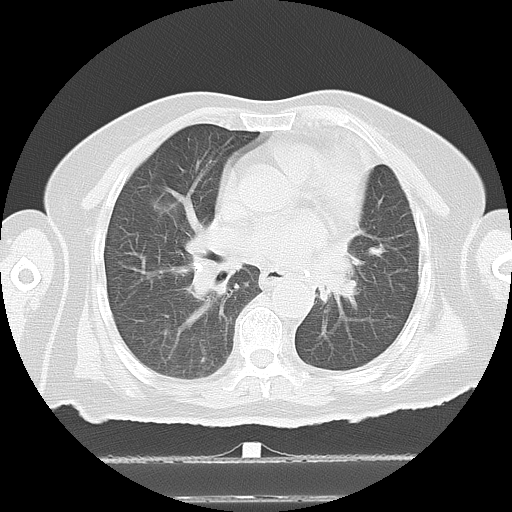
Chest CT, one axial slice; position 6 of 27 along the scan axis; reconstruction kernel LUNG; 120 kVp; lung window (W 1500 / L -600 HU); 512 × 512 image matrix, field of view 350 × 350 mm. Female patient, age 67 years. Case-level facts recorded for this patient, not image findings: clinical TNM (as recorded): T1a N1 M1c.
Structures marked on this image (rectangle marked by the reading radiologist):
- lung tumour (recorded histology: adenocarcinoma): bounding box (x1, y1, x2, y2) in pixels: (321, 252, 366, 315)